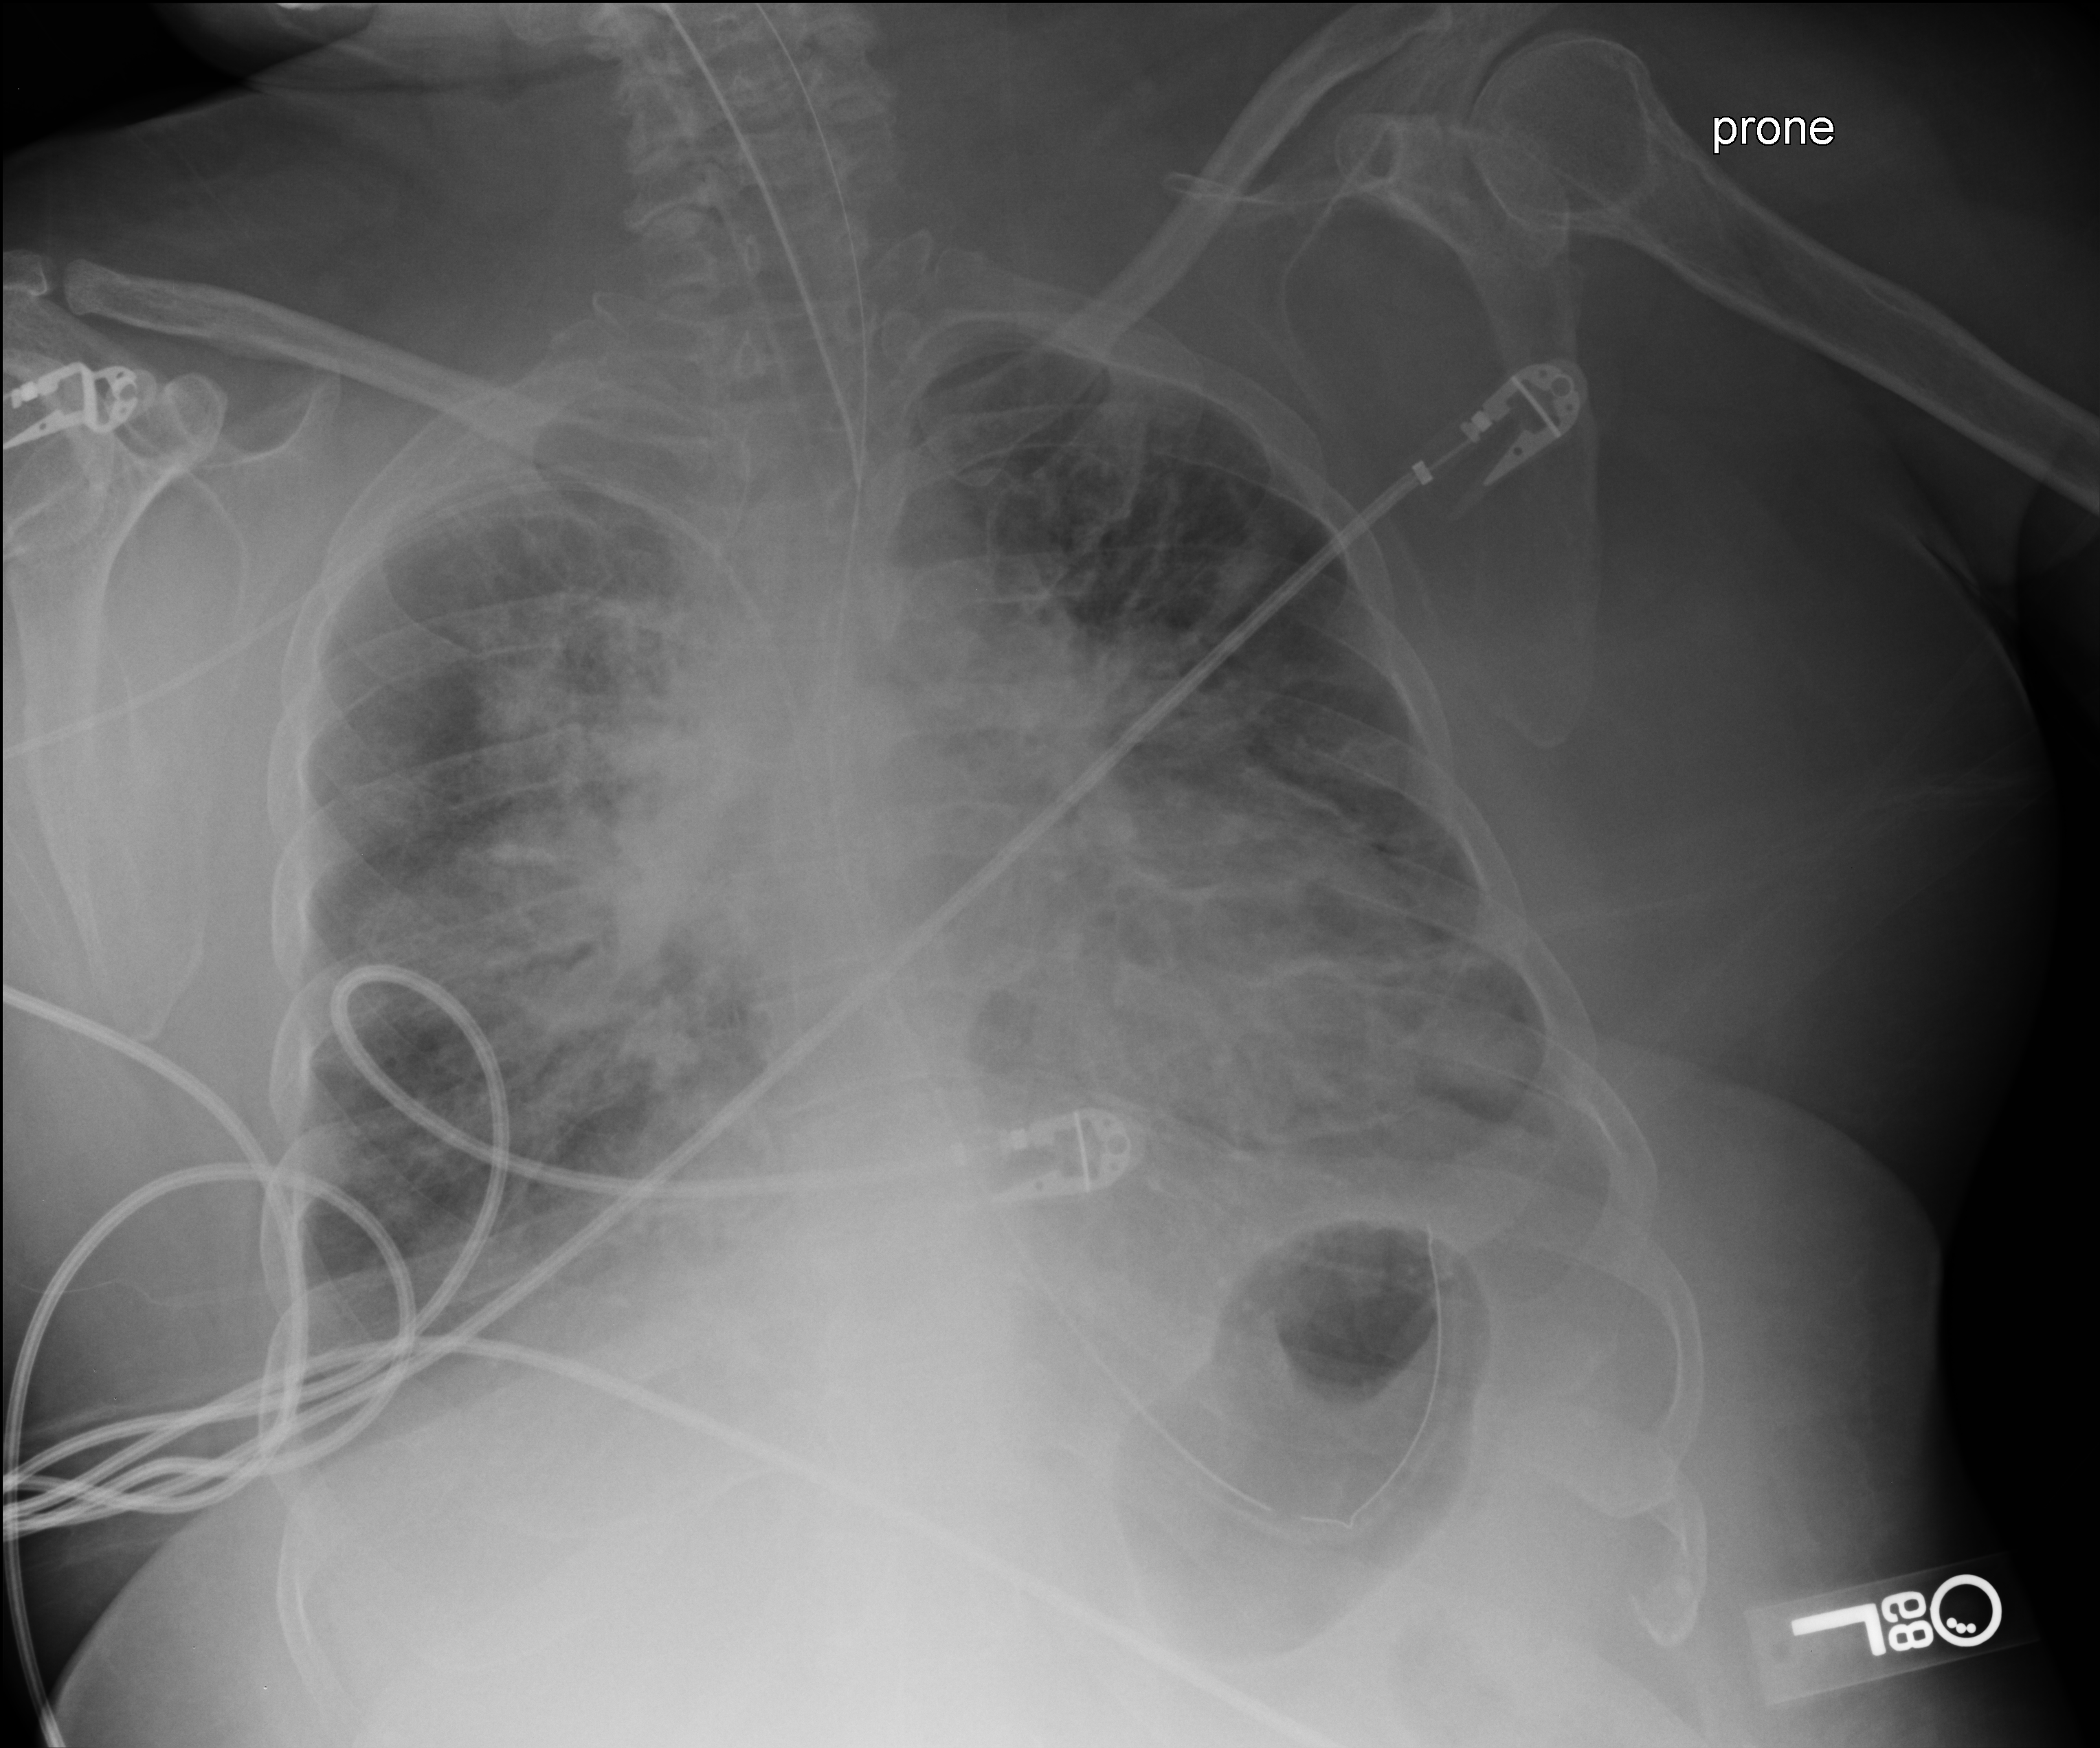
Chest X-ray (portable), anteroposterior (AP) projection. Adult patient hospitalised with COVID-19, age 18–59 years.
From the hospital-stay record, not from the radiograph (when in the stay this image was taken is not recorded):
- mechanically ventilated during this hospital stay: yes